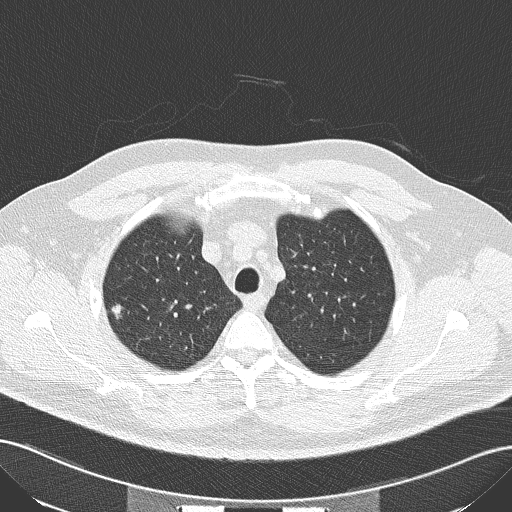
Low-dose screening chest CT, one axial slice; position 121 of 152 along the scan axis; 120 kVp; lung window (W 1500 / L -600 HU); 2 mm slice thickness; 512 × 512 image matrix, field of view 360 × 360 mm.
Annotated regions visible in this slice (manually delineated by an expert):
- lesion 1 (tumor, upper lobe of right lung): bounding box (x1, y1, x2, y2) in pixels: (111, 304, 122, 320)